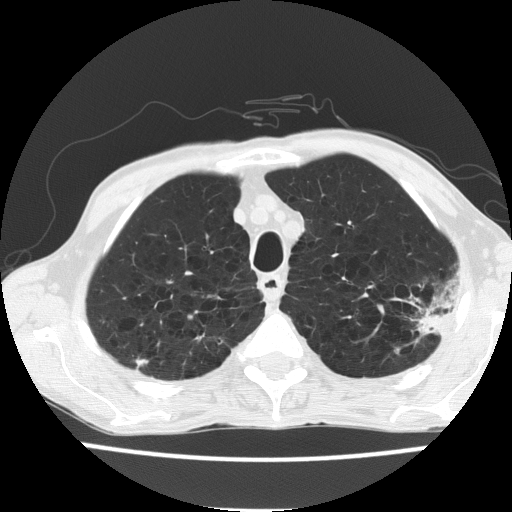
Axial slice from a low-dose chest CT screening exam, first (baseline) screen, lung window (W 1500 / L -600 HU), 2 mm slice thickness, 120 kVp, slice 37 of 187 in the series. Male participant, aged 60 years at enrolment.
Lesion marked by an expert reader, bounding box [x1, y1, x2, y2] px = [395, 278, 462, 346]. Screening reader's record for this exam: no non-calcified nodule ≥4 mm recorded. Participant outcome: lung cancer diagnosed 490 days after this screen — bronchiolo-alveolar carcinoma, mucinous, left upper lobe, stage IV (AJCC 6th edition).